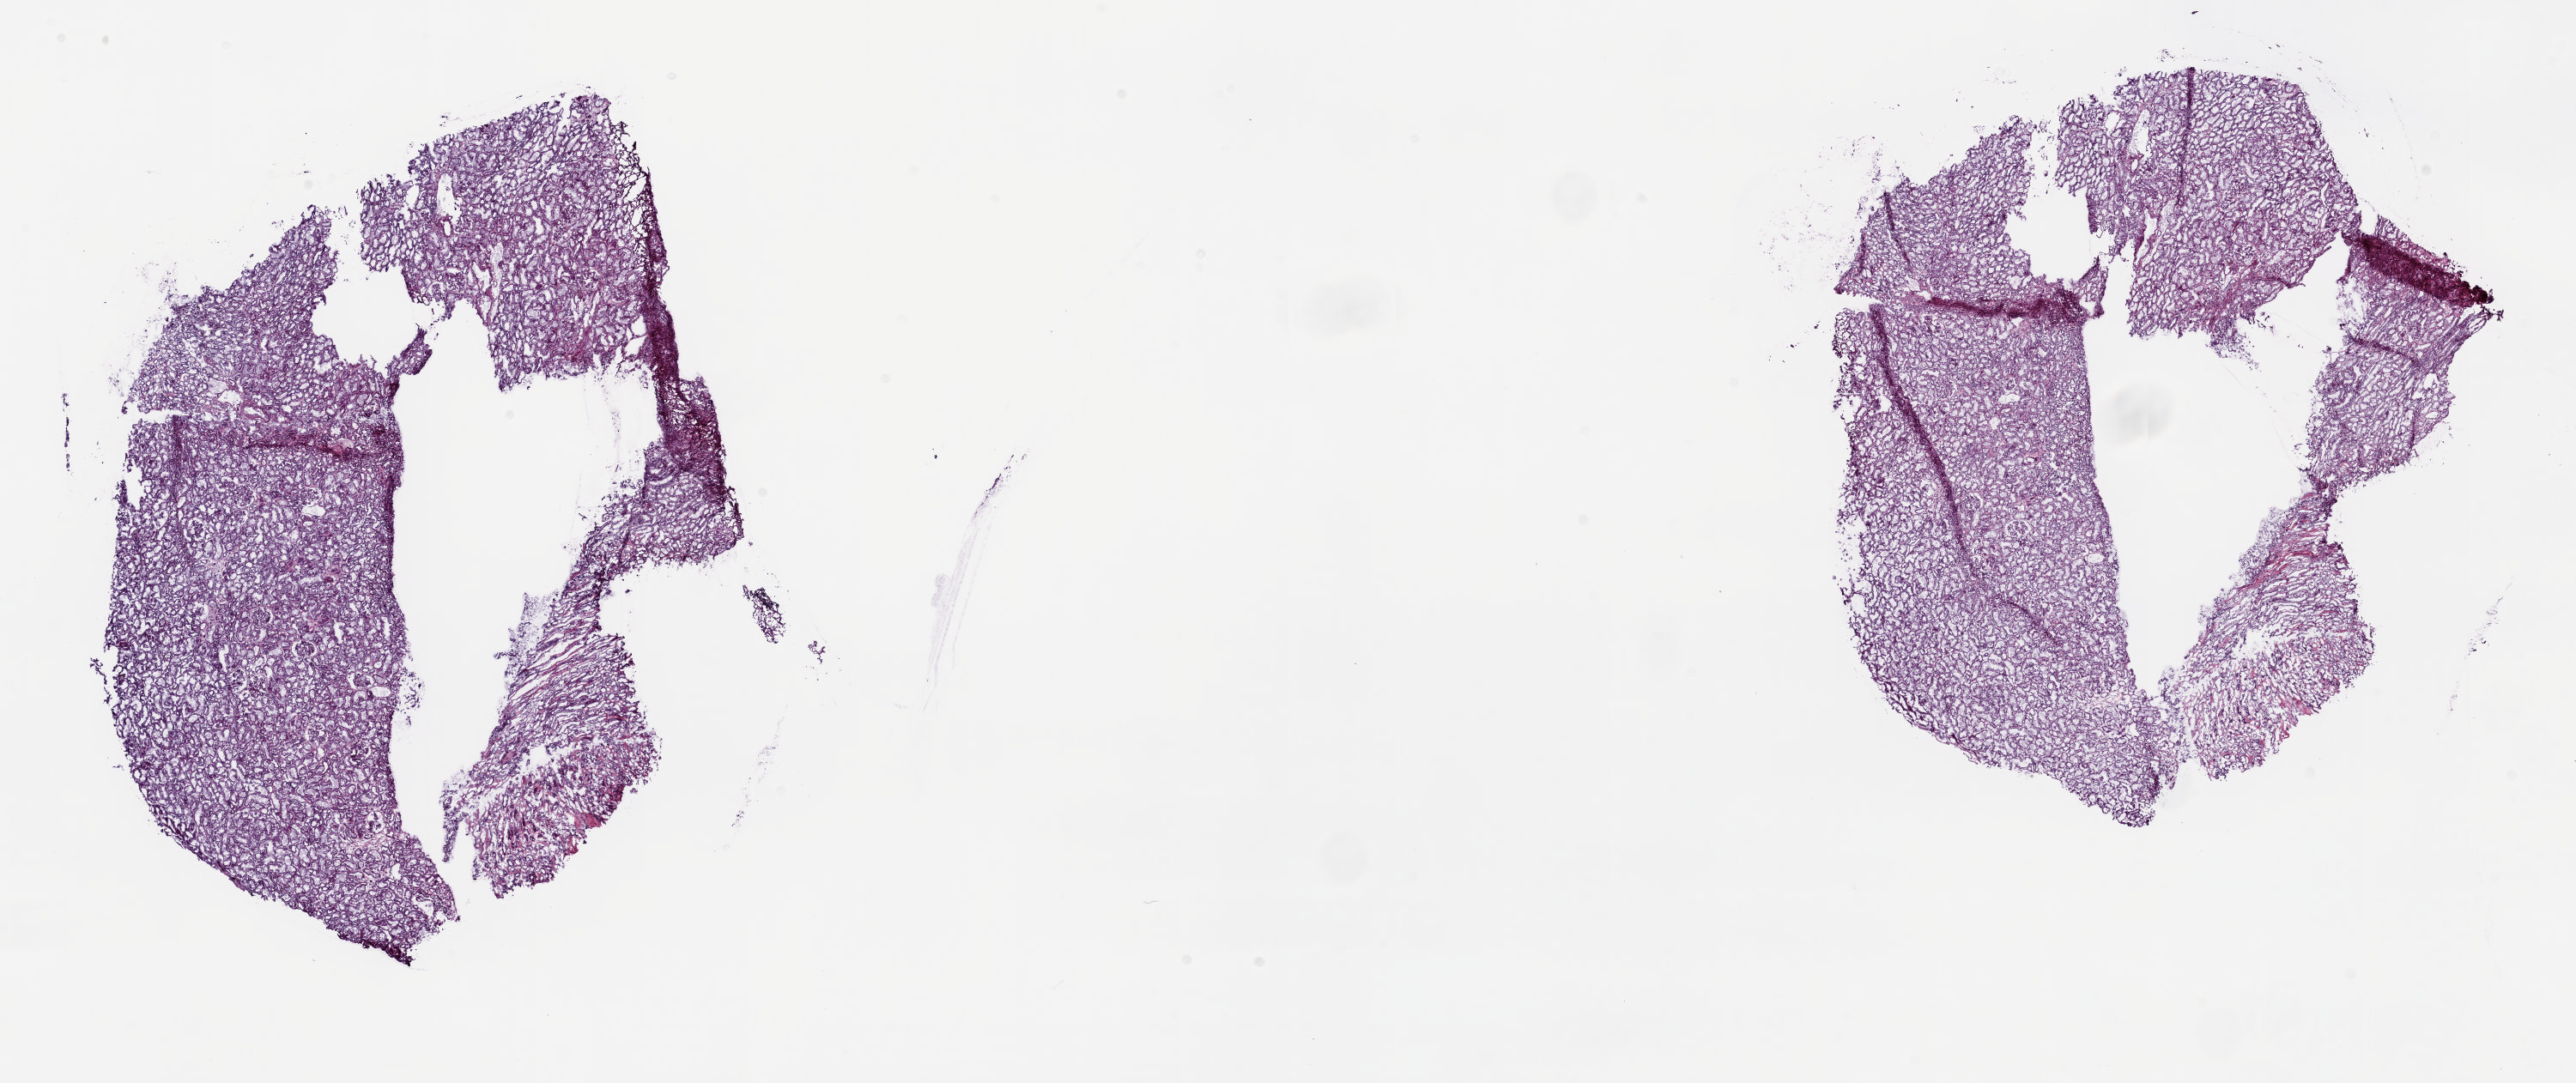
Digitized H&E tissue section (whole slide) — whole scanned area (about 23.8 x 10.0 mm) shown as a low-resolution overview, frozen section from the top of the tissue portion, kidney, solid tissue normal (non-tumour tissue) sample. Male, age 69 years at initial diagnosis. Pathologist review of this section (percent, as recorded): tumour cells 0%, tumour nuclei 0%, normal cells 60%, stromal cells 40%, necrosis 0%. Infiltration values recorded for this section: lymphocyte infiltration 3%, monocyte infiltration 1%, neutrophil infiltration 1%.
- this section: solid tissue normal sample (biorepository sample class)
- patient diagnosis: Papillary adenocarcinoma, NOS